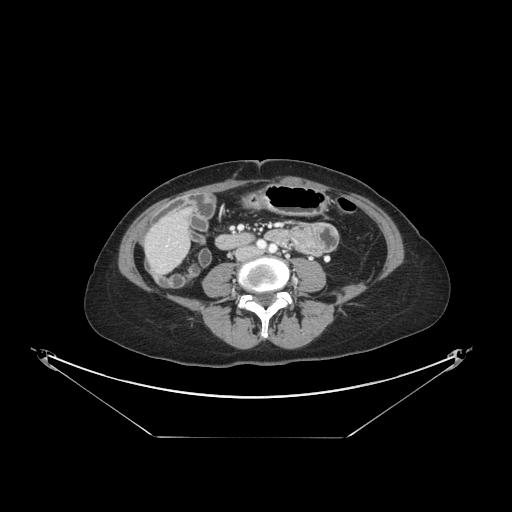
Contrast-enhanced abdominal CT, one axial slice; position 27 of 148 along the scan axis; reconstruction kernel STANDARD; 120 kVp; intravenous contrast given; soft-tissue window (W 400 / L 40 HU); 2.5 mm slice thickness; 512 × 512 image matrix, field of view 500 × 500 mm. Female patient, age 73 years. From the clinical record (not read from this slice): diagnosis: colorectal cancer liver metastases, imaged before liver resection; multiple liver metastases: no; largest metastasis: 1 cm; disease in both lobes: no.
Outlined on this slice (outlined manually by an expert reader):
- liver: box from (x=149, y=212) to (x=189, y=271) px
- planned liver remnant (the part of the liver to remain after resection): (x=166, y=211)–(x=187, y=235)